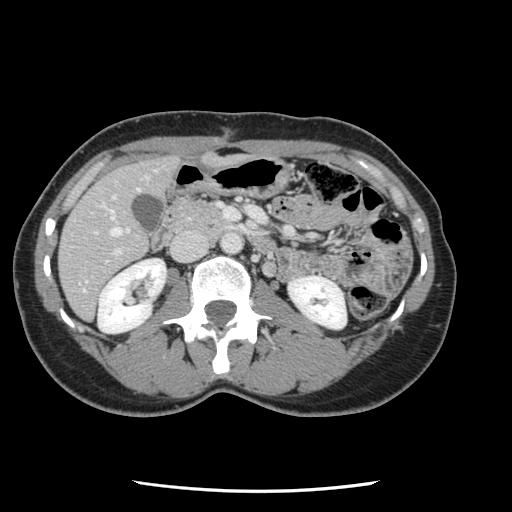
Contrast-enhanced abdominal CT, one axial slice; position 40 of 134 along the scan axis; intravenous contrast given; soft-tissue window (W 400 / L 40 HU); 512 × 512 image matrix, field of view 330 × 330 mm. Female patient, age 43 years. From the clinical record (not read from this slice): diagnosis: colorectal cancer liver metastases, imaged before liver resection; multiple liver metastases: yes; largest metastasis: 3.4 cm; chemotherapy before resection: no.
Outlined on this slice (outlined manually by an expert reader):
- hepatic veins: box from (x=110, y=189) to (x=140, y=237) px
- liver: (x=60, y=157)–(x=179, y=319)
- planned liver remnant (the part of the liver to remain after resection): (x=59, y=157)–(x=179, y=319)
- portal vein (with intrahepatic branches): (x=93, y=202)–(x=265, y=263)